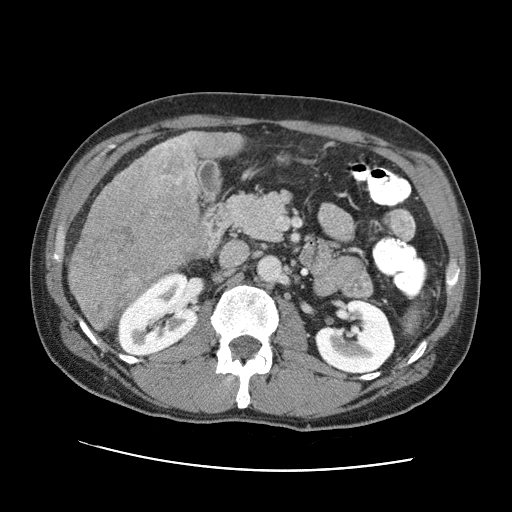
Contrast-enhanced abdominal CT (liver protocol), one axial slice. Slice 29 of 95 in the series (ordered by position). Reconstruction kernel STANDARD. One of 2 acquisitions stored at this slice position. Soft-tissue window (W 400 / L 40 HU). 512 × 512 image matrix, field of view 360 × 360 mm. From the clinical record (not read from this slice): diagnosis: hepatocellular carcinoma (patient treated with transarterial chemoembolisation; whether this scan precedes or follows treatment is not stated here); TNM stage (as recorded): Stage-IVA; Child-Pugh class: A; tumour nodularity: multinodular.
Annotated regions visible in this slice (semi-automatic segmentation, software-assisted and operator-edited):
- liver parenchyma outside the tumour (the mass and vessels are separate outlines, so this box may not span the whole liver): bounding box <68,132,226,265> (left, top, right, bottom; pixels)
- mass: <66,138,203,332>
- liver vessels: <181,135,220,244>